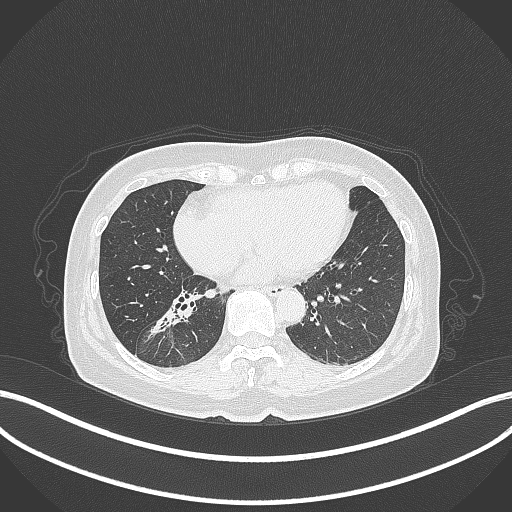
Chest CT, one axial slice. Position 150 of 429 along the scan axis. Reconstruction kernel B70f. Lung window (W 1500 / L -600 HU). 1 mm slice thickness. 512 × 512 image matrix. Female patient, age 67 years. Case-level facts recorded for this patient, not image findings: clinical TNM (as recorded): T1c N1 M0.
Outlined on this slice (rectangle marked by the reading radiologist):
- lung tumour (recorded histology: adenocarcinoma): bounding box (x1, y1, x2, y2) in pixels: (140, 290, 198, 343)